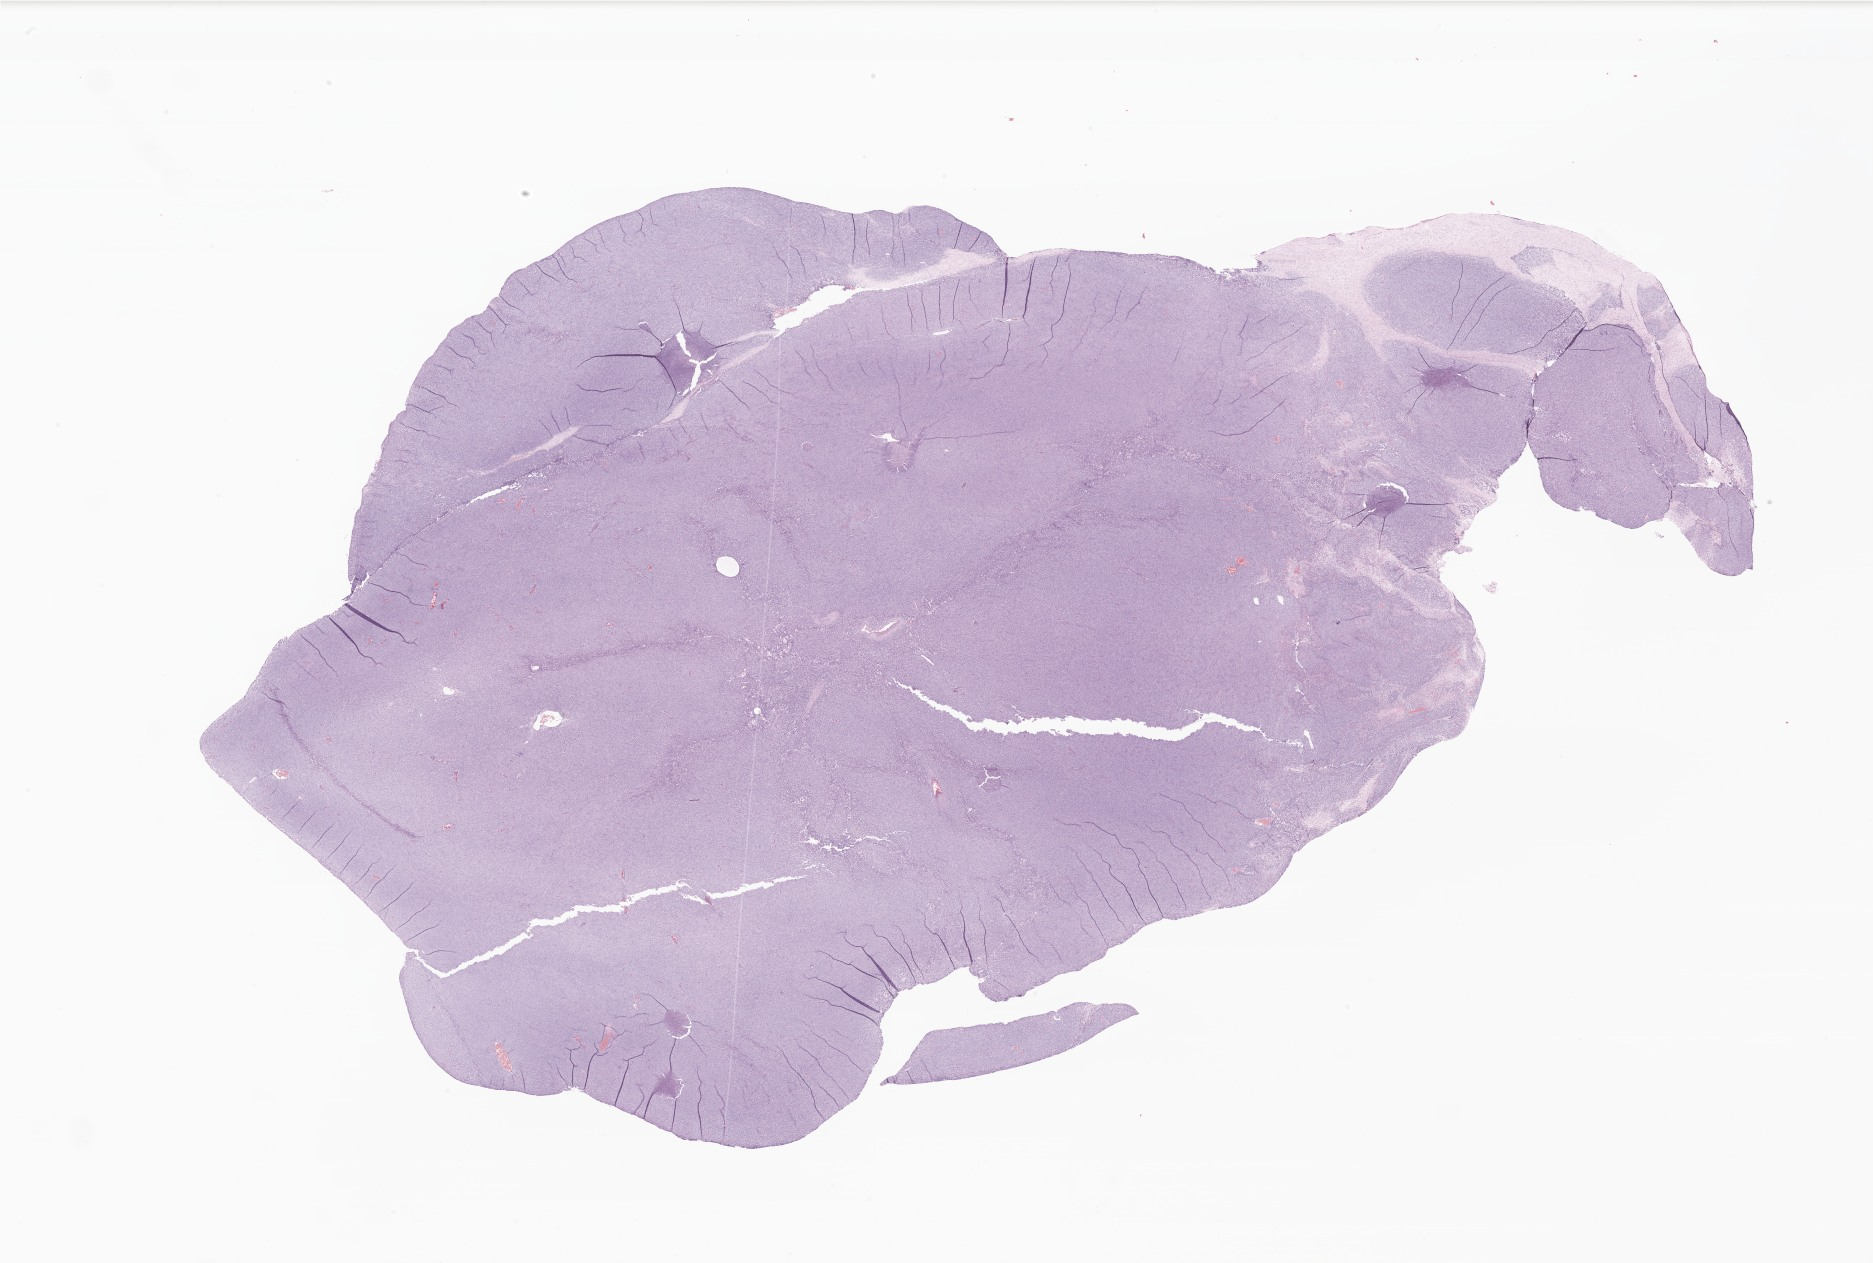
Digitized haematoxylin and eosin-stained section of tumor tissue from the kidney, whole scanned area (about 31.6 x 21.3 mm) shown as a low-resolution overview; FFPE section. Female patient, age 921 days (about 2.5 years).
* recorded diagnosis: Clear cell sarcoma of kidney